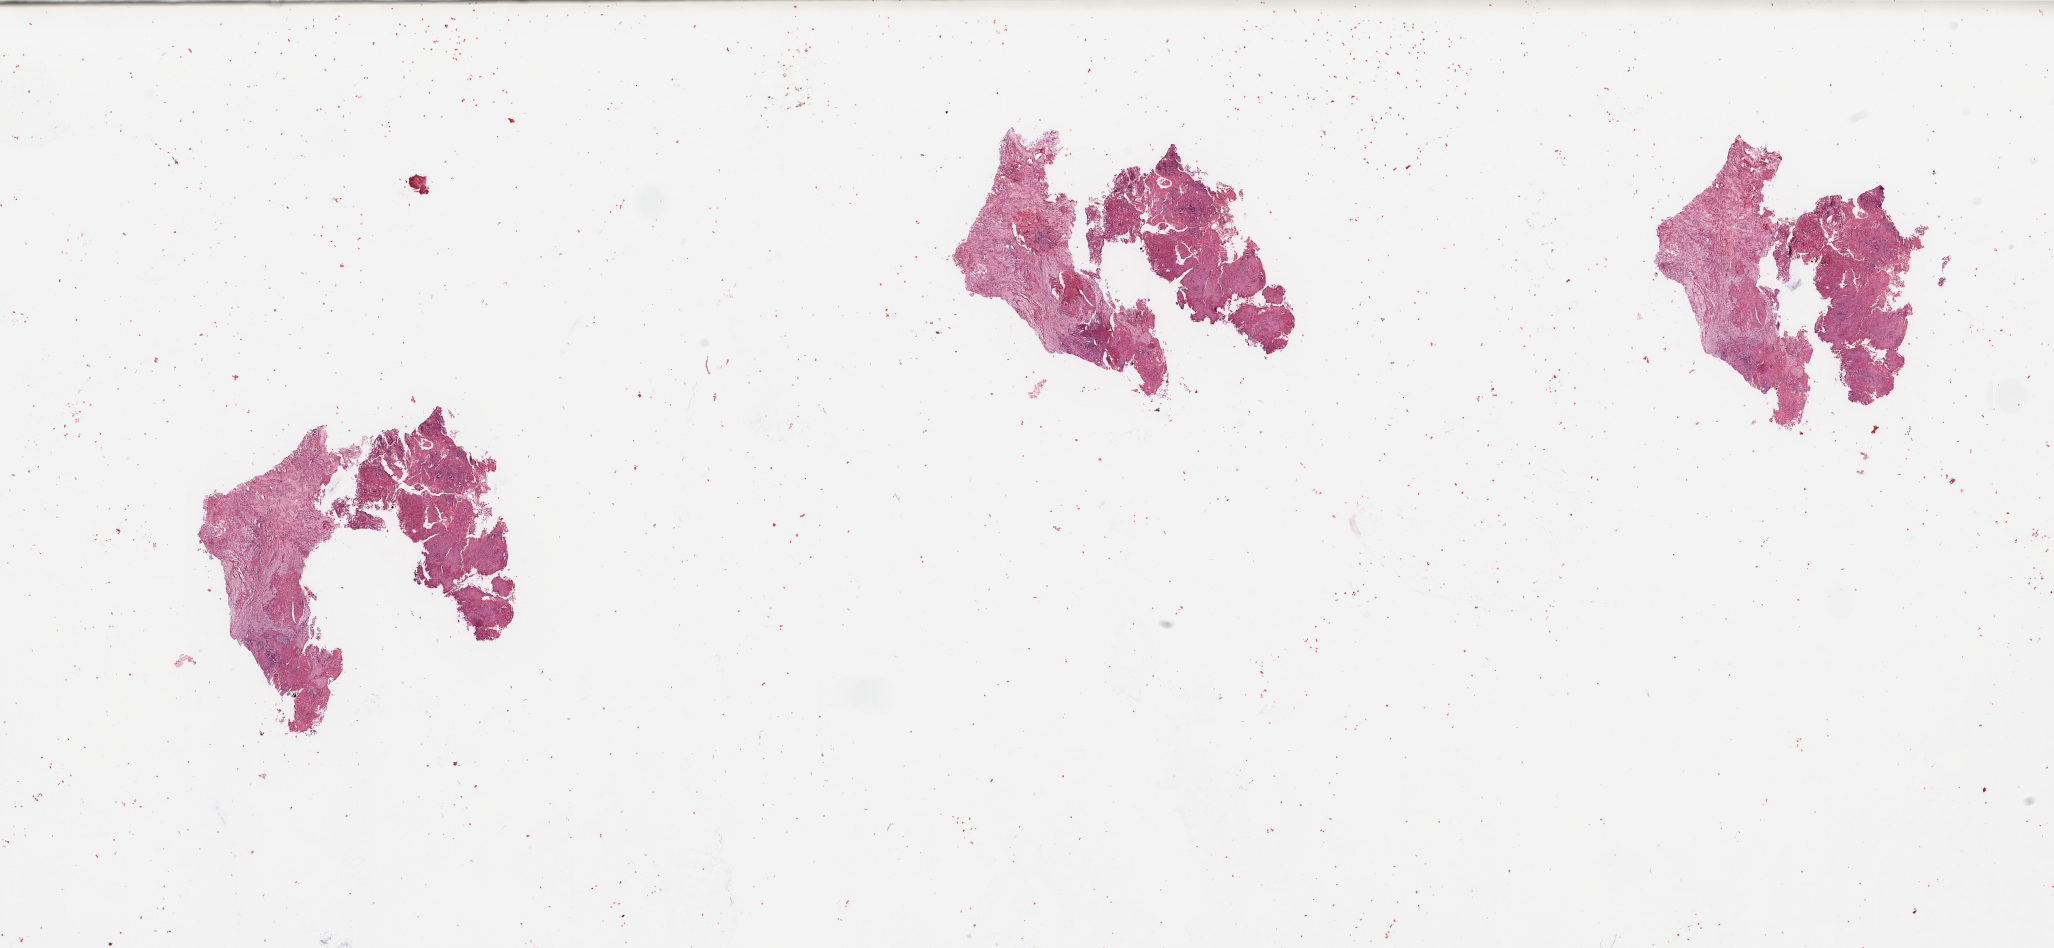
H&E whole-slide image, low-resolution overview of the scanned area, about 32.5 x 15.0 mm; tumour tissue sample, sampled site: lung. Male, 70 y/o. Composition of this section per pathologist review: tumour nuclei 70%, necrosis 5%.
Diagnosis: Squamous cell carcinoma, NOS.